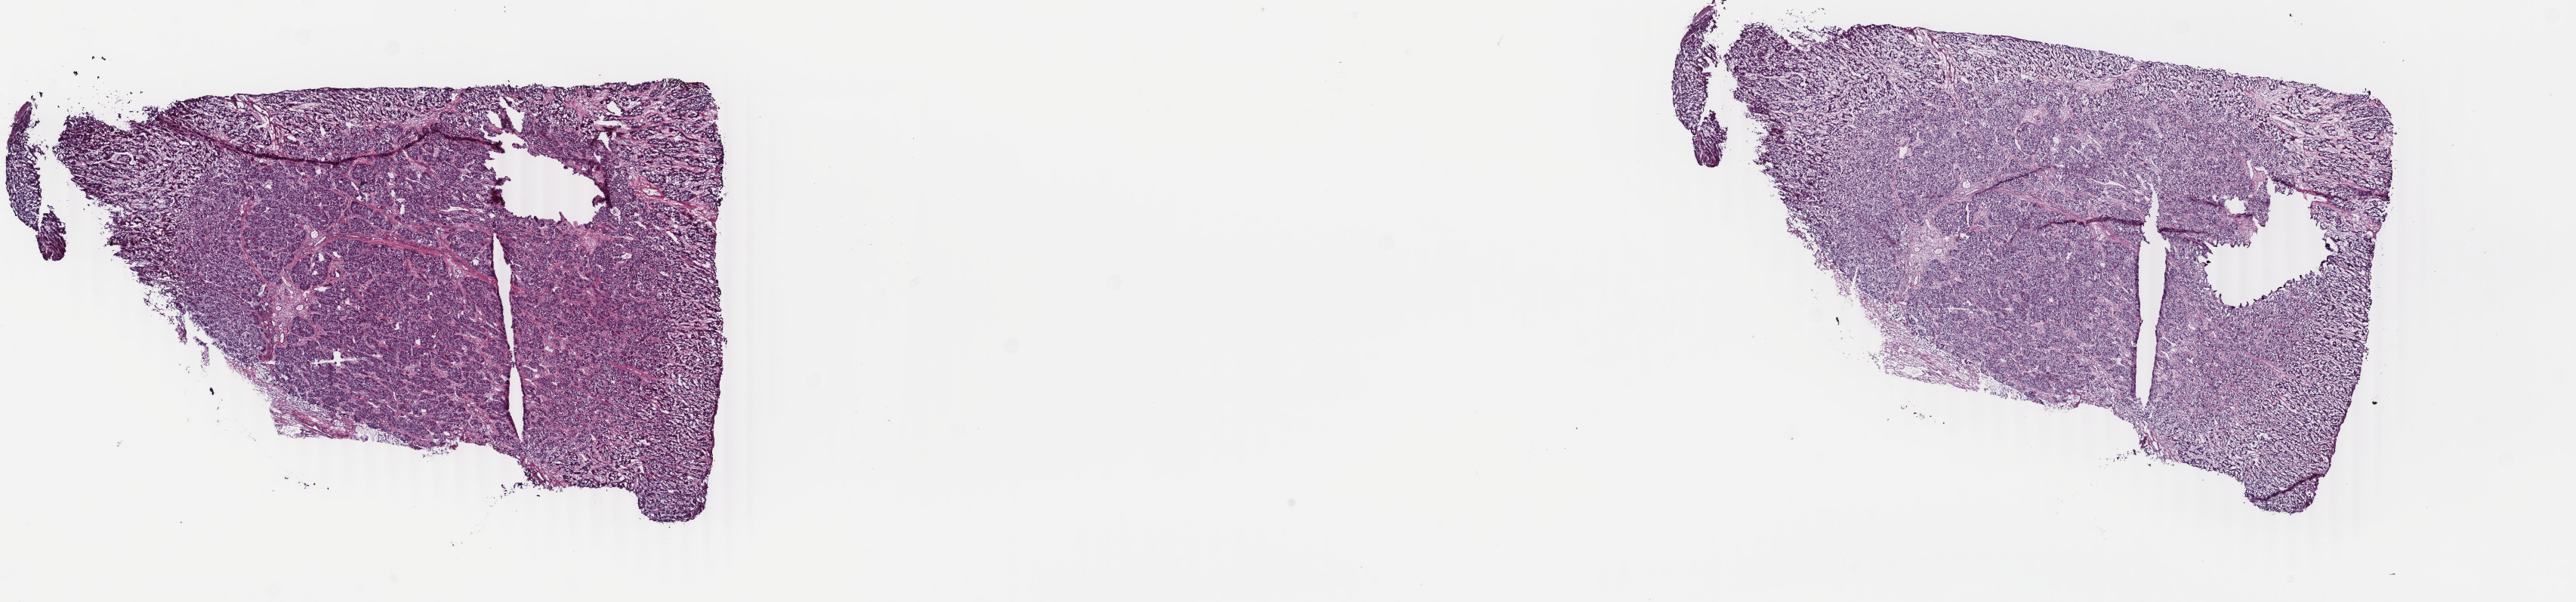
Digitized H&E tissue section (whole slide) — whole scanned area (about 27.1 x 6.3 mm) shown as a low-resolution overview; frozen section from the top of the tissue portion; primary tumour sample from the liver. Male patient; age at initial diagnosis 40 years. Histologic grade: G3 (poorly differentiated). Slide review estimates, as recorded: tumour cells 95%, tumour nuclei 95%, normal cells 0%, stromal cells 5%, necrosis 0%. Inflammatory infiltration, as recorded: lymphocyte infiltration 1%, monocyte infiltration 0%, neutrophil infiltration 0%.
- AJCC pathologic stage: IV
- histologic diagnosis: Hepatocellular carcinoma, NOS